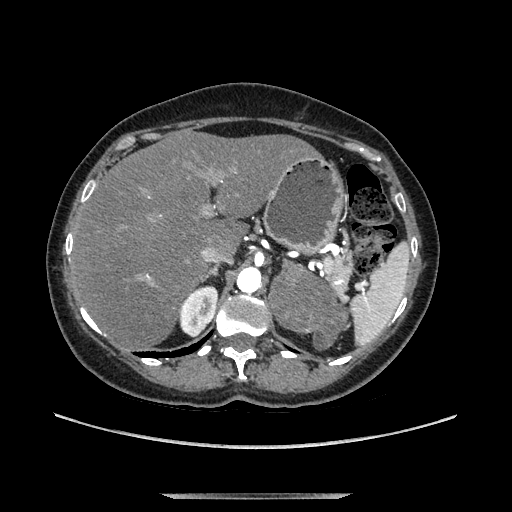
Contrast-enhanced abdominal CT, one axial slice; slice 89 of 169 in the series (ordered by position); soft-tissue window (W 400 / L 40 HU); 1.25 mm slice thickness; 512 × 512 image matrix. Female patient. Case-level facts recorded for this patient, not image findings: diagnosis: adrenocortical carcinoma; tumour side: left adrenal; tumour size at pathology: 9 cm; Ki-67 index: 2 %; stage (as recorded): 3.
Structures marked on this image (semi-automatic segmentation, software-assisted and operator-edited):
- mass: bounding box (x1, y1, x2, y2) in pixels: (272, 263, 346, 347)